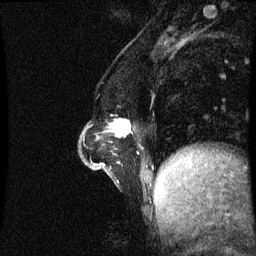
Breast MRI (dynamic contrast-enhanced), one sagittal slice. Position 20 of 60 along the scan axis. Dynamic contrast-enhanced series, image 2 of 3 at this slice position (ordered by acquisition). 1.5 T. TE 4.2 ms, TR 8.9 ms. 256 × 256 image matrix, field of view 200 × 200 mm. Female patient, age 47 years. Case-level facts recorded for this patient, not image findings: setting: breast cancer imaged before/during neoadjuvant chemotherapy; receptor status: HR-positive, HER2-negative.
Structures marked on this image (semi-automatic segmentation, software-assisted and operator-edited):
- analysis volume of interest (the breast-tissue region the enhancement analysis was run in; not a lesion): bounding box [x1, y1, x2, y2] px = [81, 114, 132, 163]
- tumour enhancement mask (voxels above the 70 % enhancement threshold inside the analysis volume of interest): [113, 120, 131, 137]